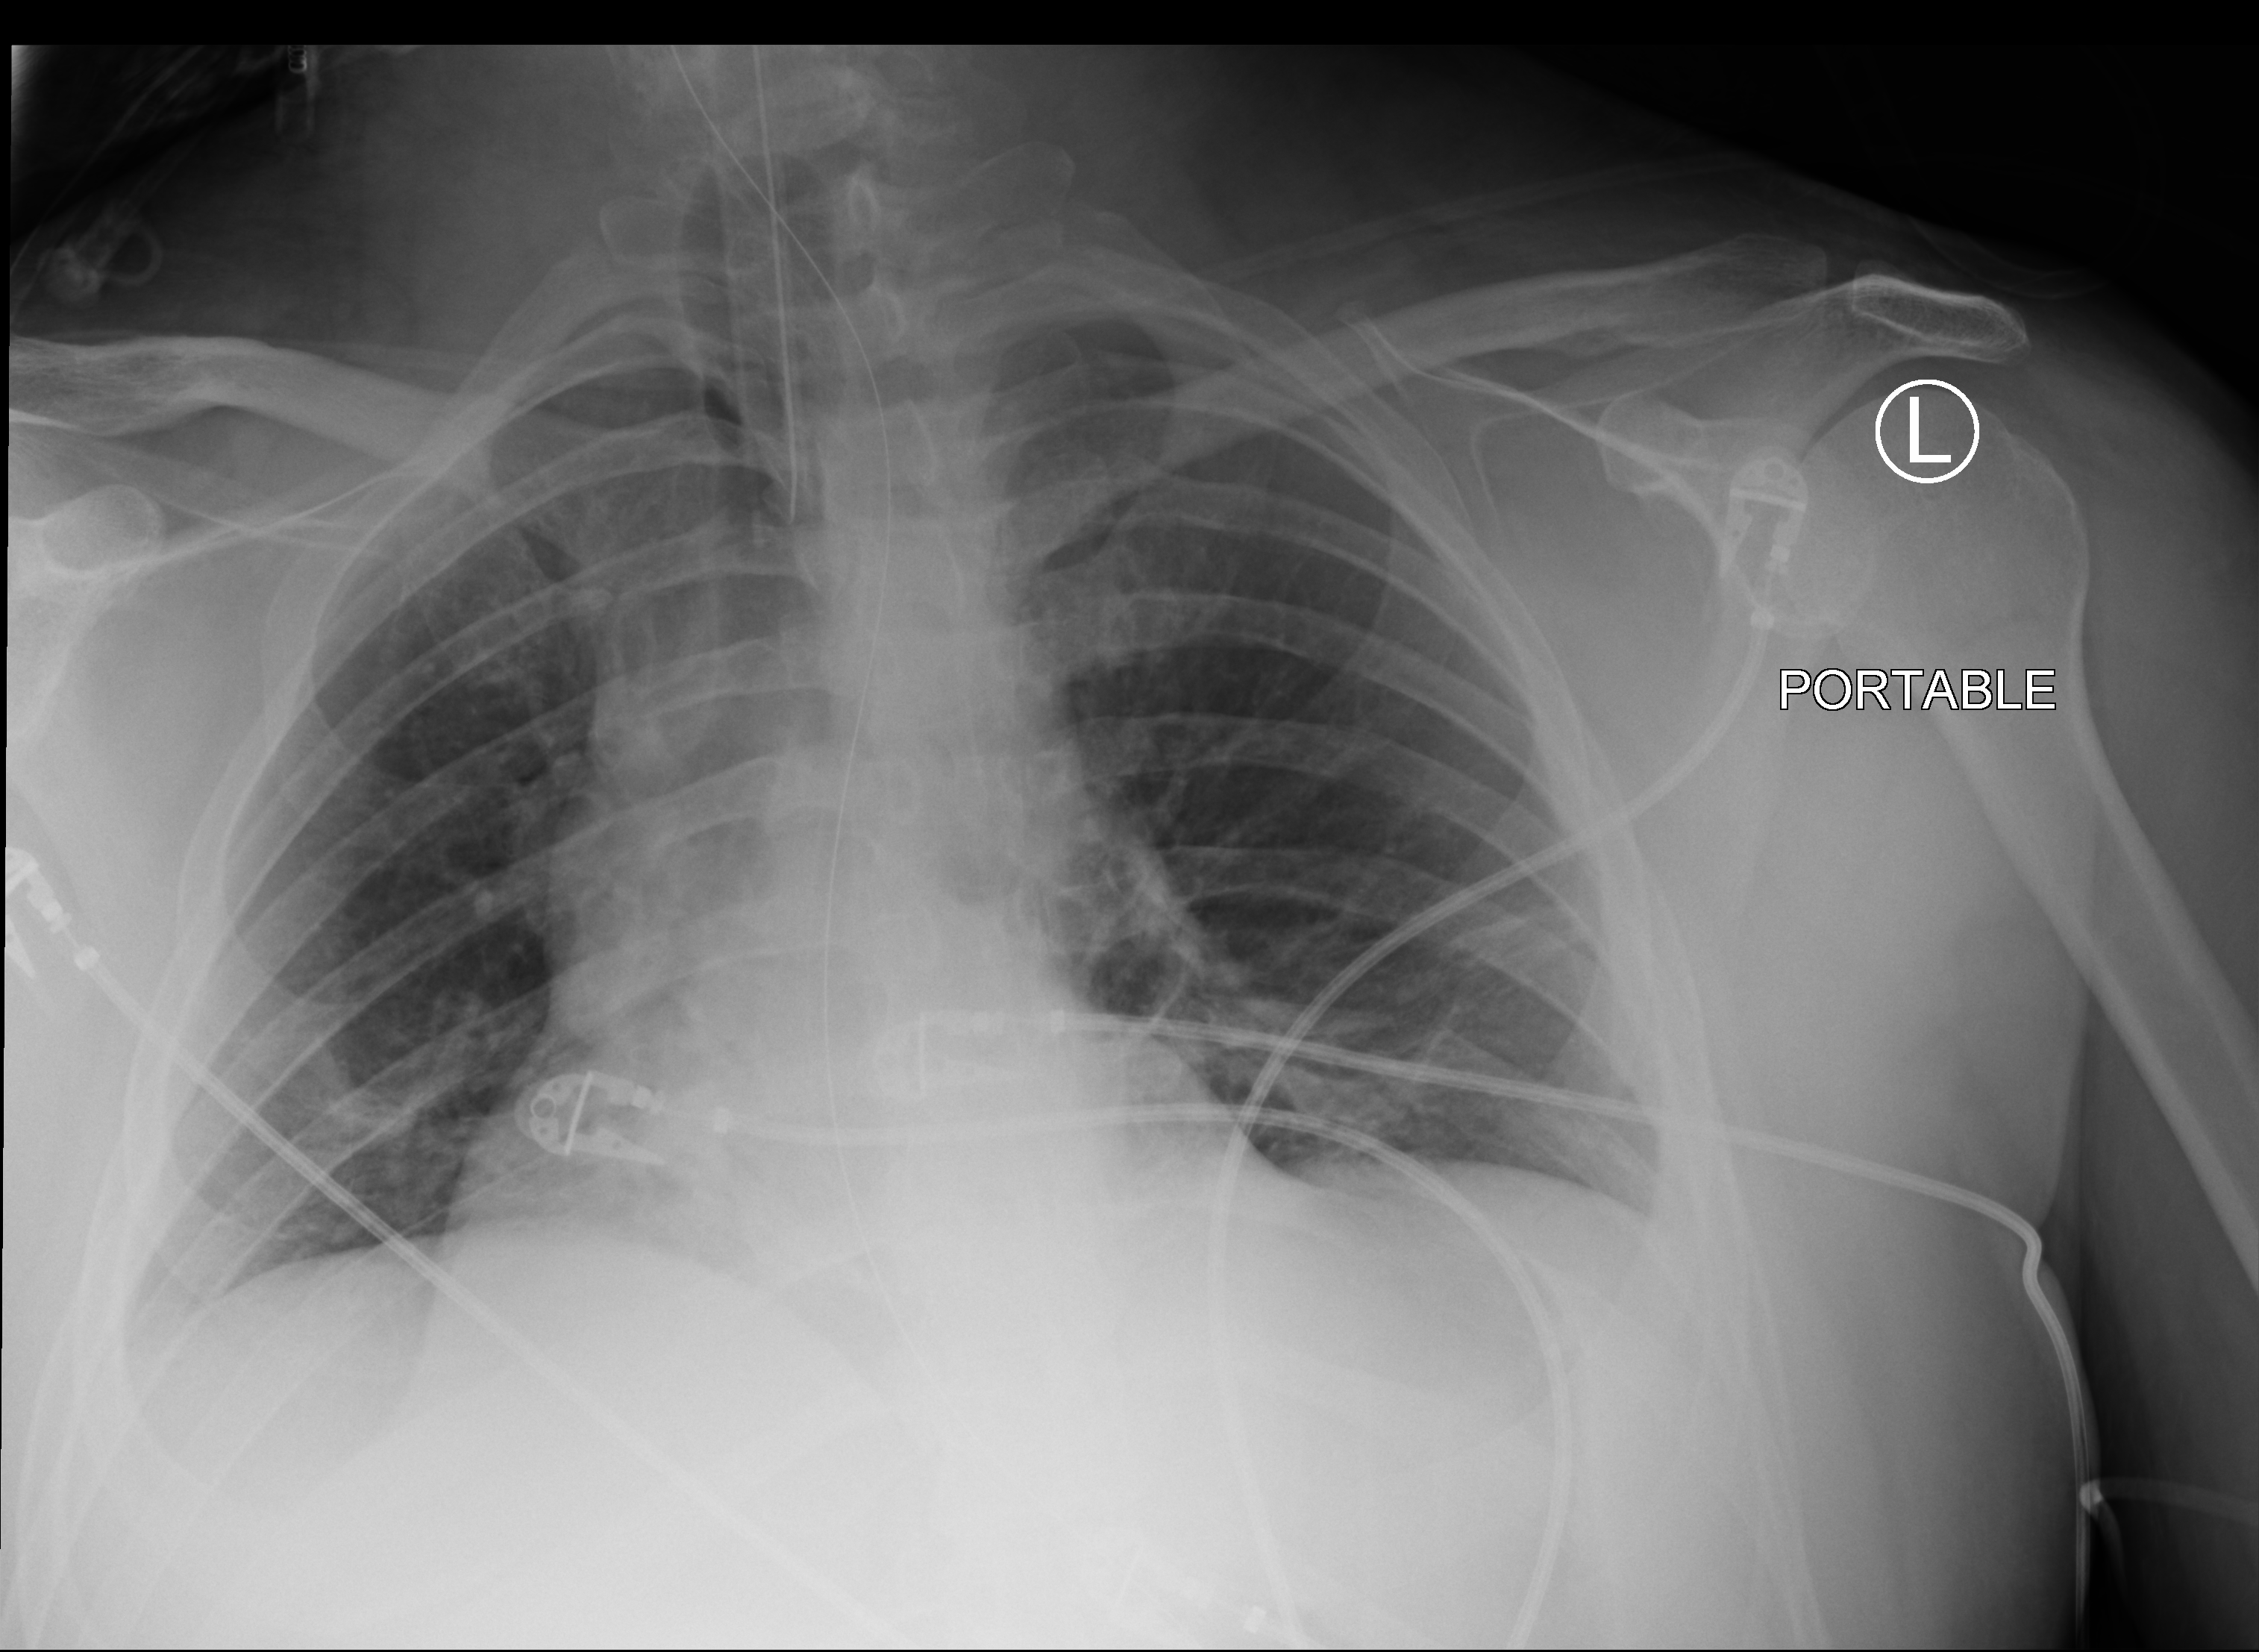
Chest X-ray (portable); anteroposterior (AP) projection. Patient hospitalised with COVID-19; male, aged 18–59 years.
From the hospital-stay record, not from the radiograph (when in the stay this image was taken is not recorded): admitted to intensive care during this hospital stay: yes; mechanically ventilated during this hospital stay: yes.